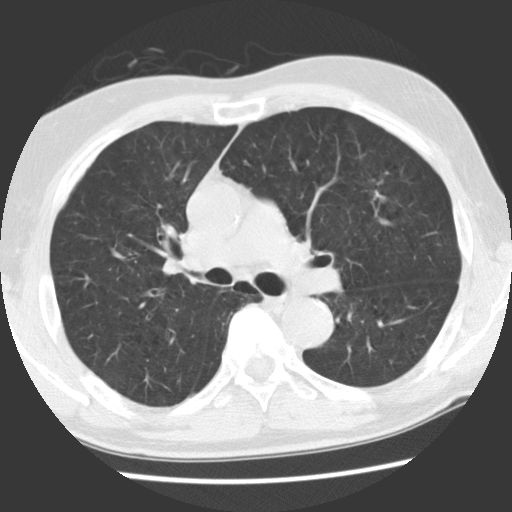
Axial slice from a low-dose chest CT screening exam. First (baseline) screen. Lung window (W 1500 / L -600 HU). Slice 80 of 131 in the series. Male, age 70 years at enrolment.
Lesion marked by an expert reader, bounding box <348,176,401,223> (left, top, right, bottom; pixels). The screening reader recorded 2 non-calcified nodules or masses ≥4 mm on this exam (left upper lobe, right lower lobe); which of them this box marks is not recorded. Official screen result: positive, change unspecified: nodule(s) >= 4 mm or enlarging nodule(s), mass(es), or other non-specific abnormalities suspicious for lung cancer. Later outcome: lung cancer diagnosed 879 days after this screen (after the third annual screen) — adenocarcinoma, NOS, left upper lobe, moderately differentiated (G2), stage IIIA (AJCC 6th edition), 17 mm at pathology.